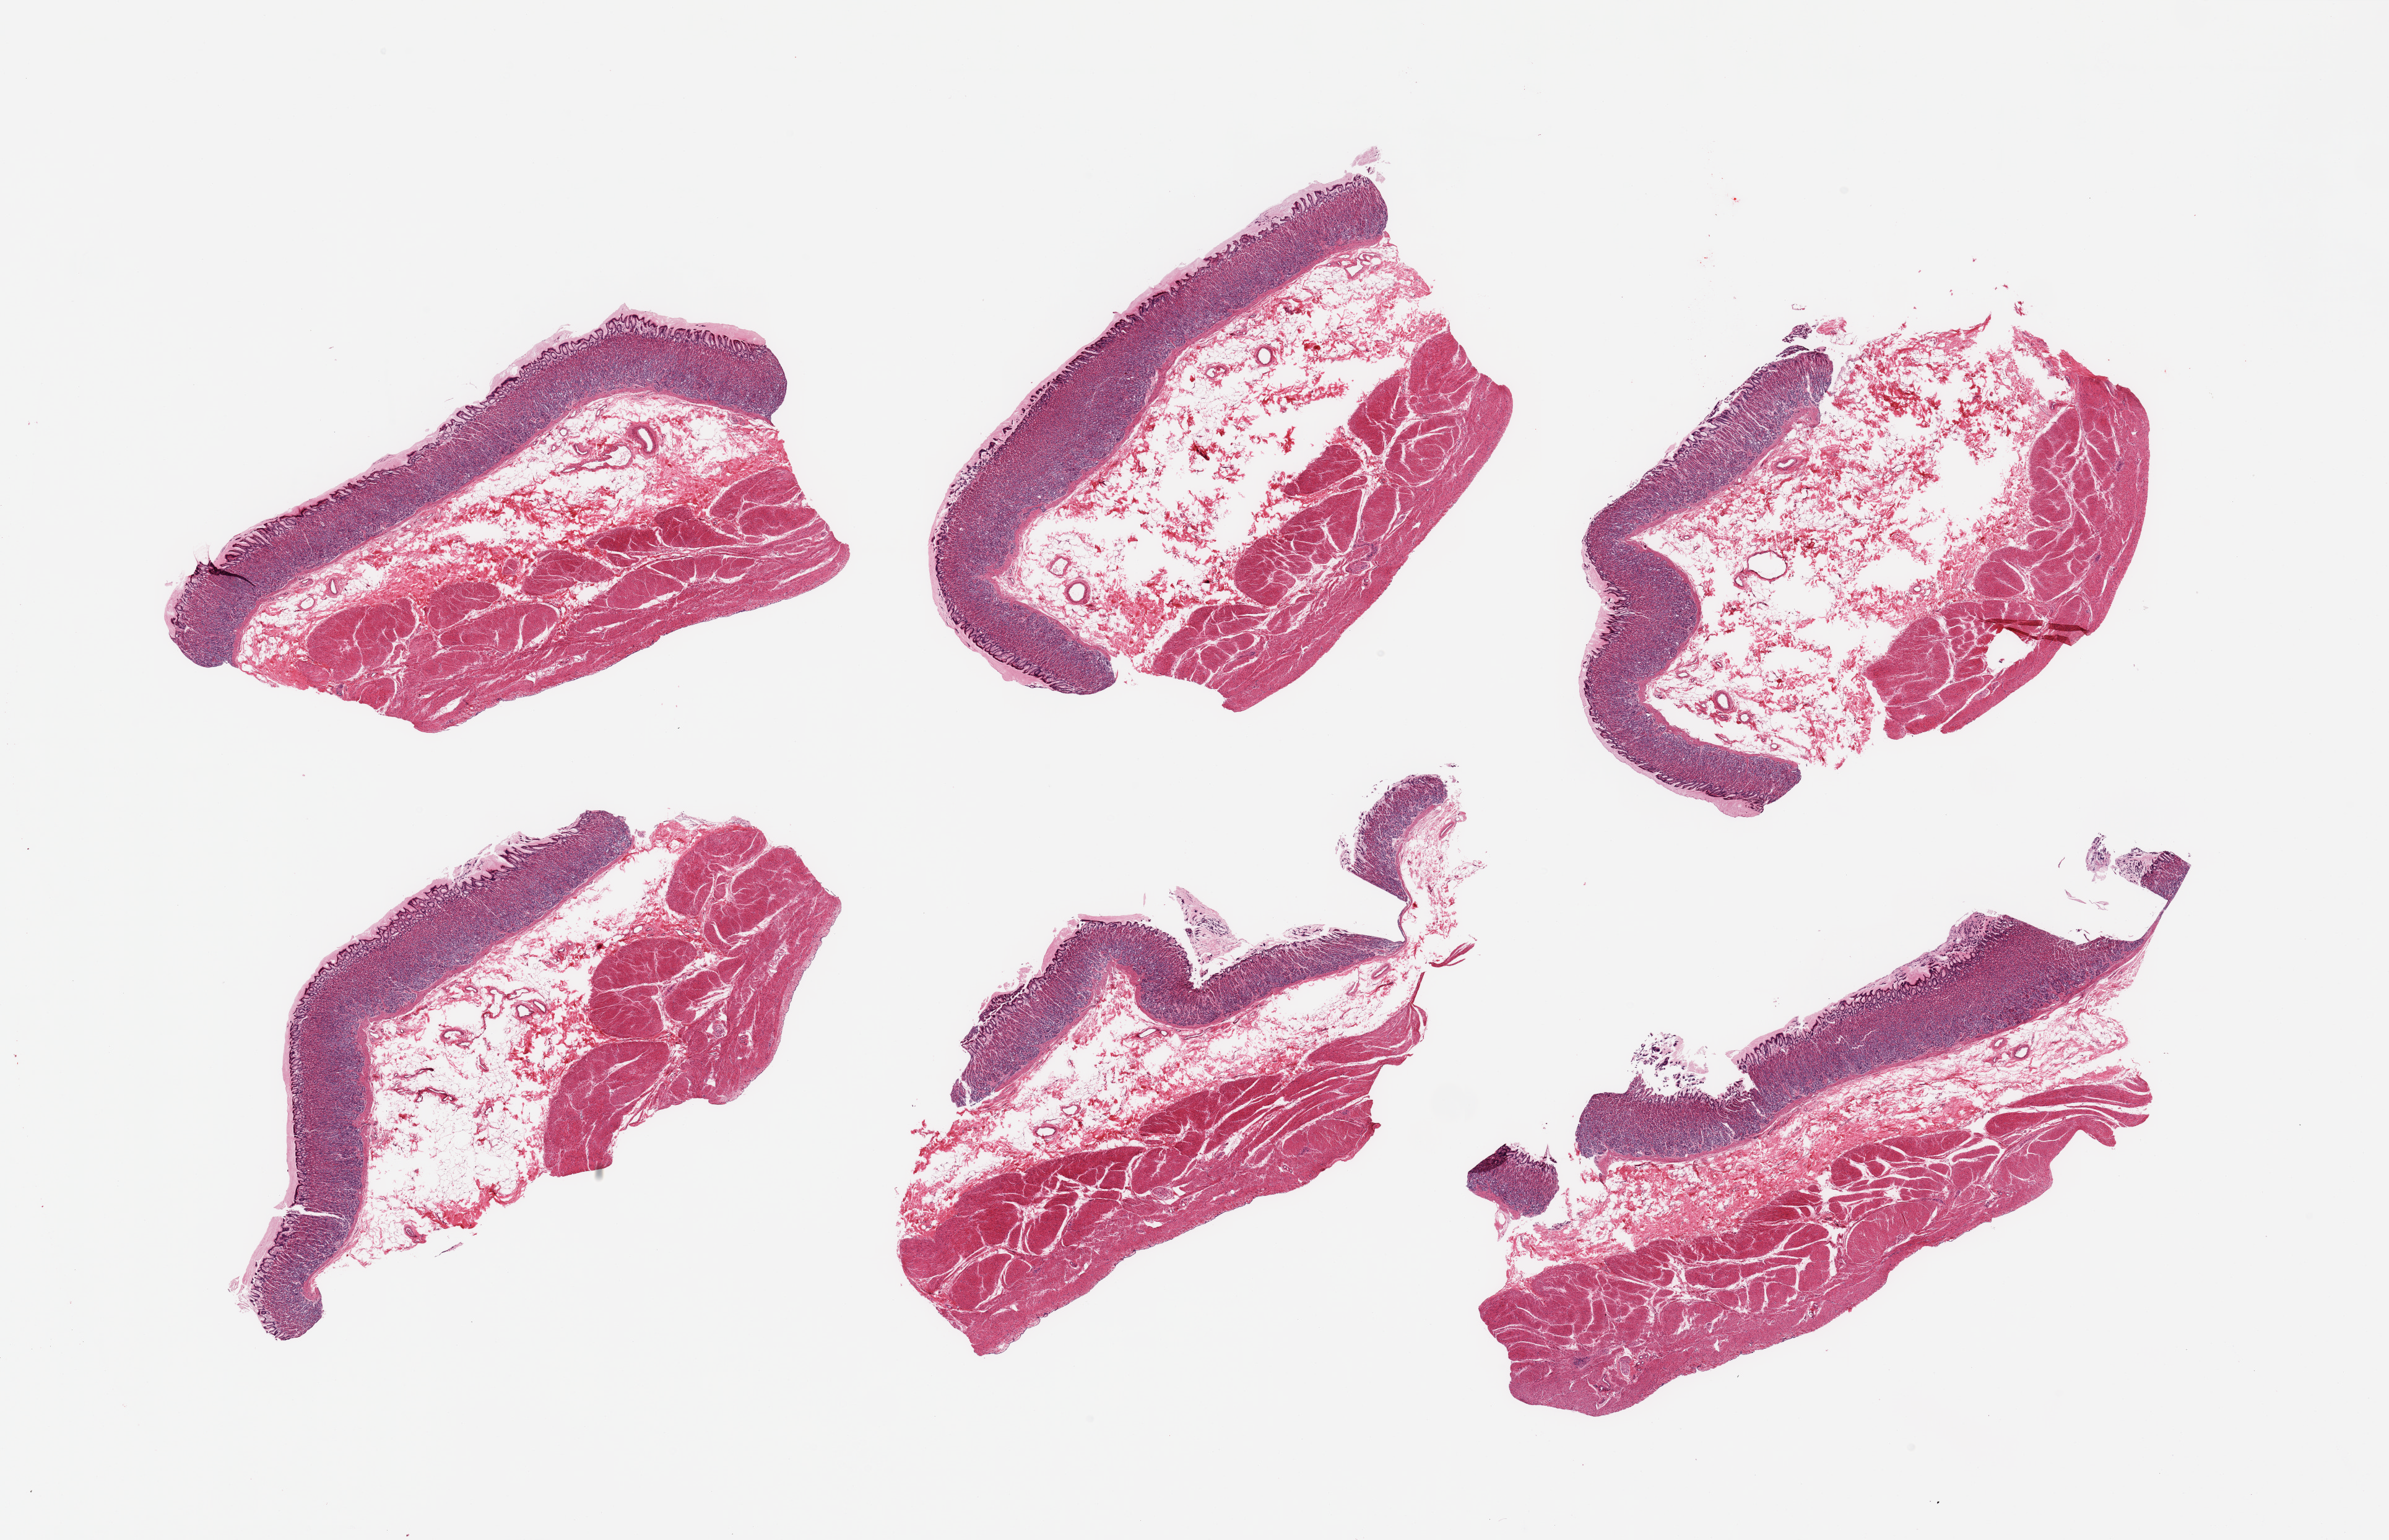
Digitized H&E-stained section — a low-resolution overview of the entire scanned area, about 30.5 x 19.7 mm (acquisition: 20x scan). PAXgene-fixed, paraffin-embedded tissue. Target tissue: stomach. Tissue donor sample. Donor: female.
Review note (as recorded): 6 pieces, well preserved mucosa up to ~`1mm, ~20-25% thickness.